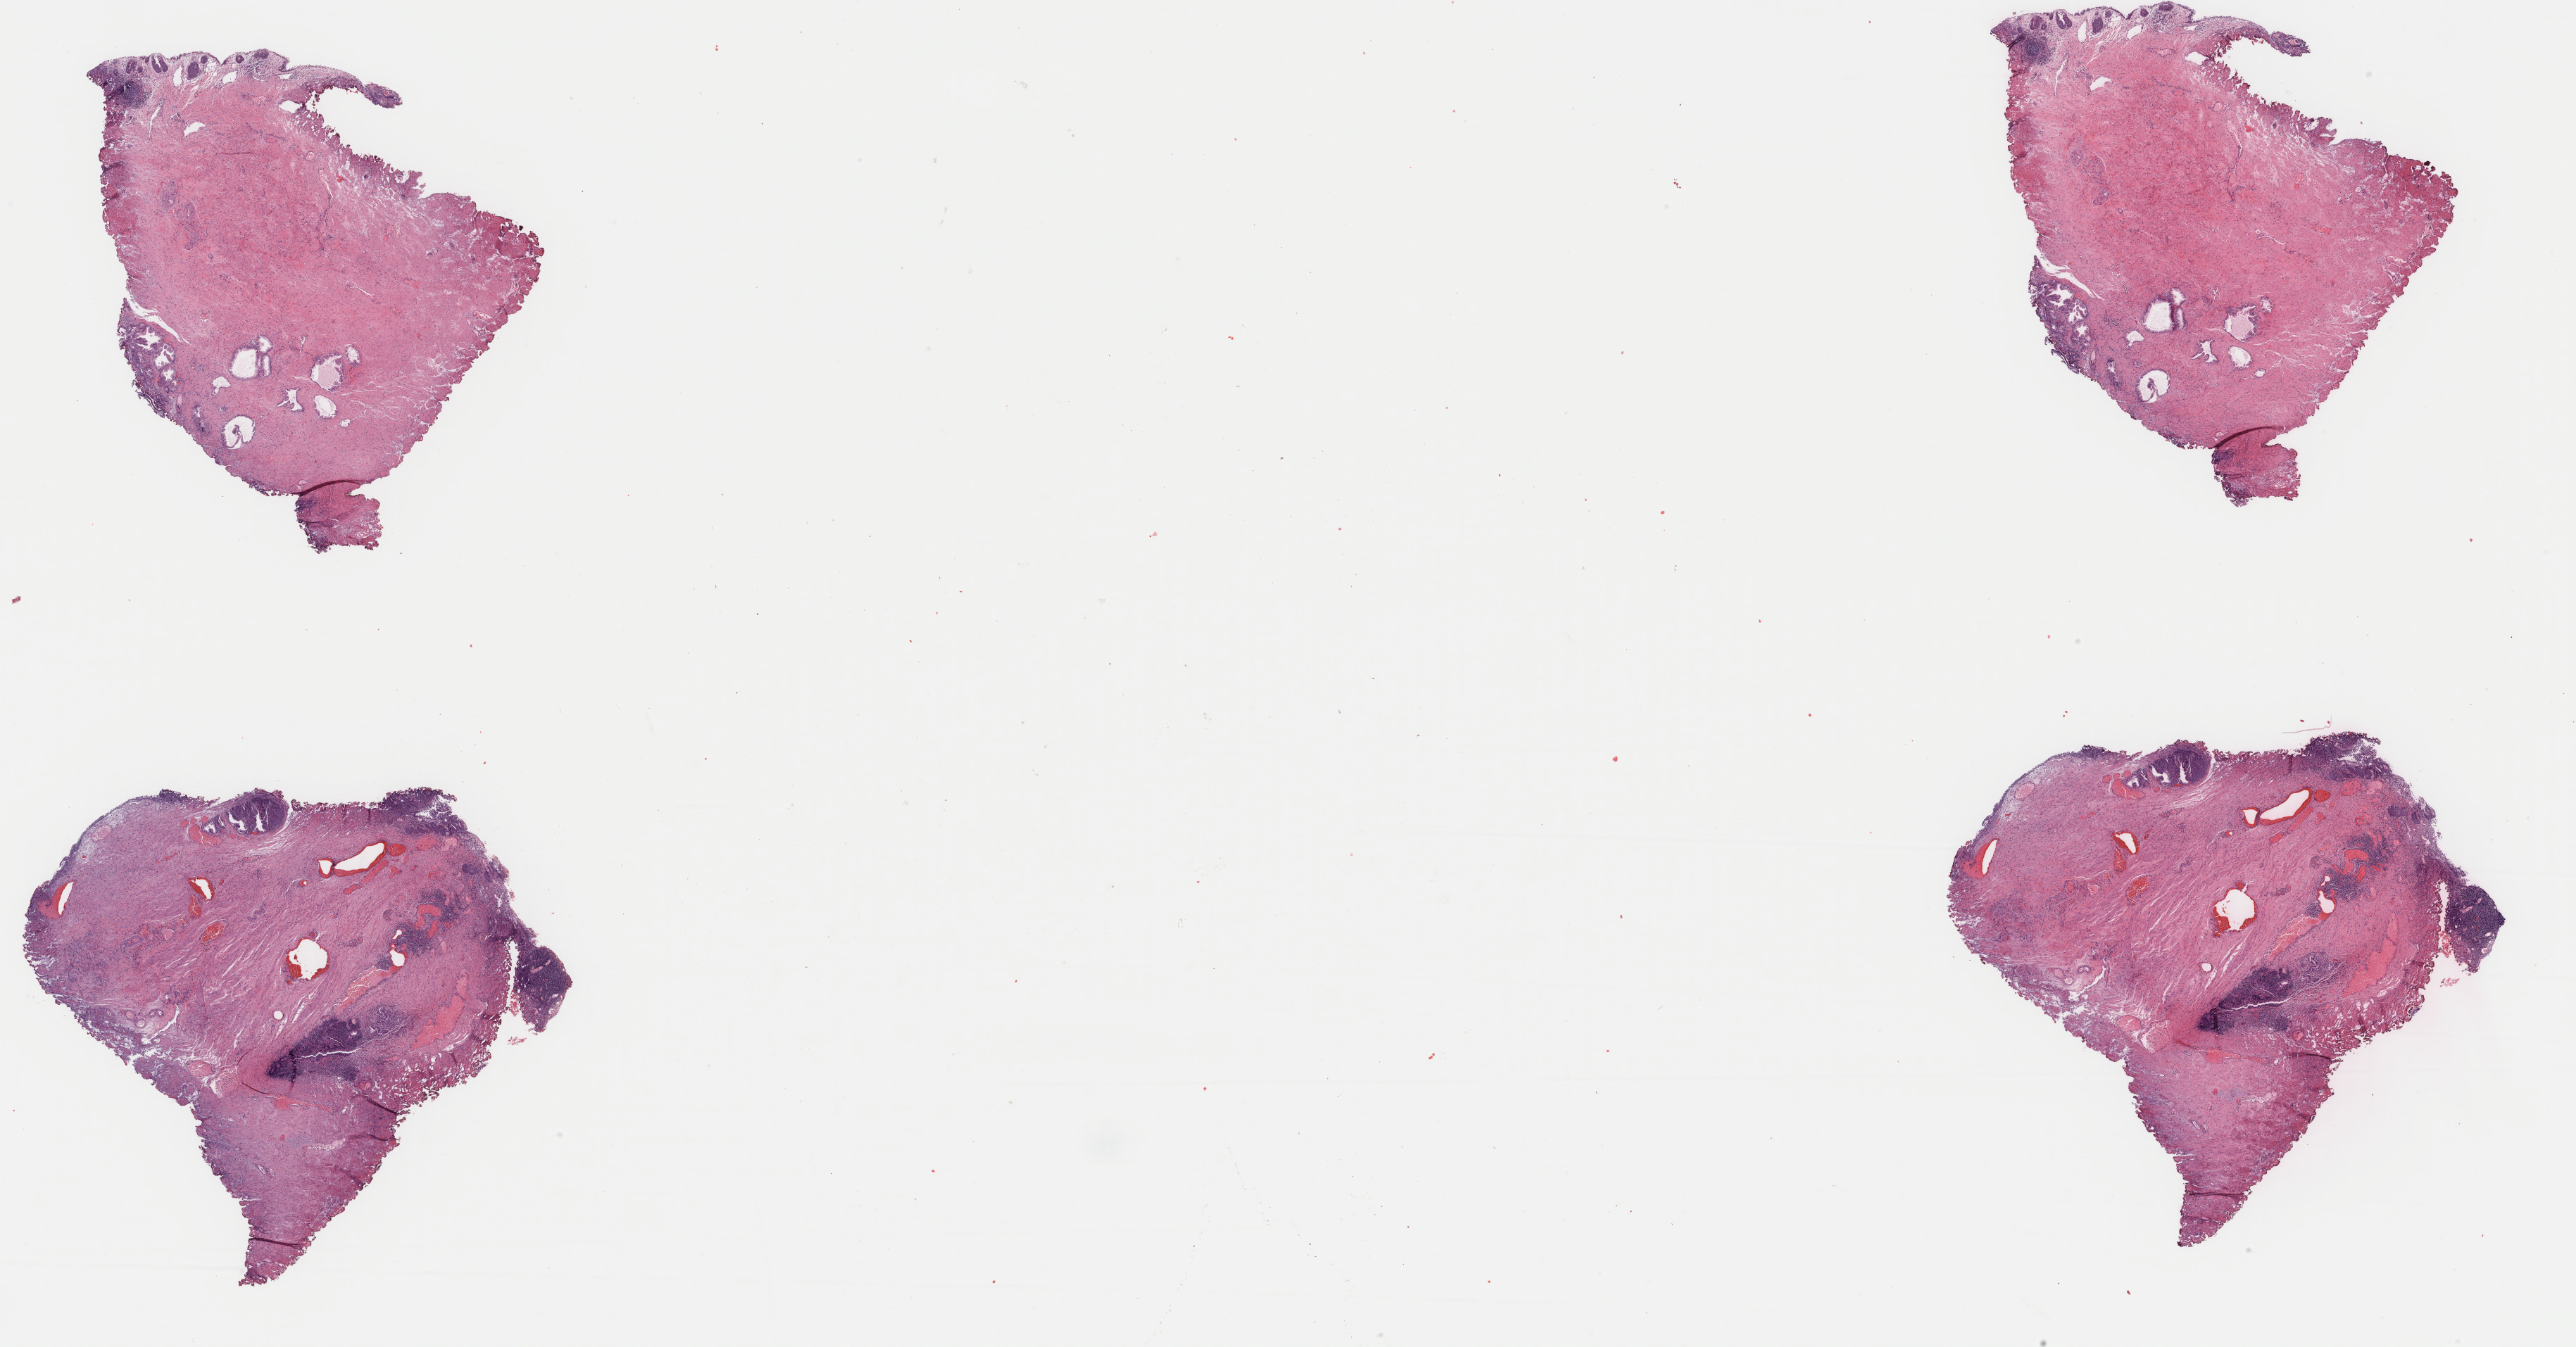
Digitized H&E tissue section (whole slide), low-resolution overview of the scanned area, about 29.0 x 15.2 mm (acquisition: 40x scan), formalin-fixed paraffin-embedded (FFPE) diagnostic section, primary tumour sample from the bladder. Male patient; age at initial diagnosis 66 years. Histologic grade: high grade.
• AJCC pathologic stage: II (6th edition)
• TNM: NX MX
• pathologic diagnosis: Transitional cell carcinoma